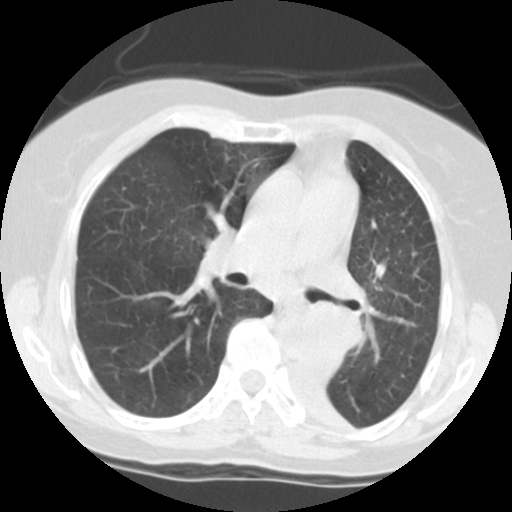
Low-dose screening chest CT, one axial slice; slice 71 of 113 in the series (ordered by position); 140 kVp; lung window (W 1500 / L -600 HU); 512 × 512 image matrix, field of view 280 × 280 mm.
Structures marked on this image (expert manual segmentation):
- lesion 1 (tumor, left main bronchus): bounding box (x1, y1, x2, y2) in pixels: (278, 301, 365, 360)